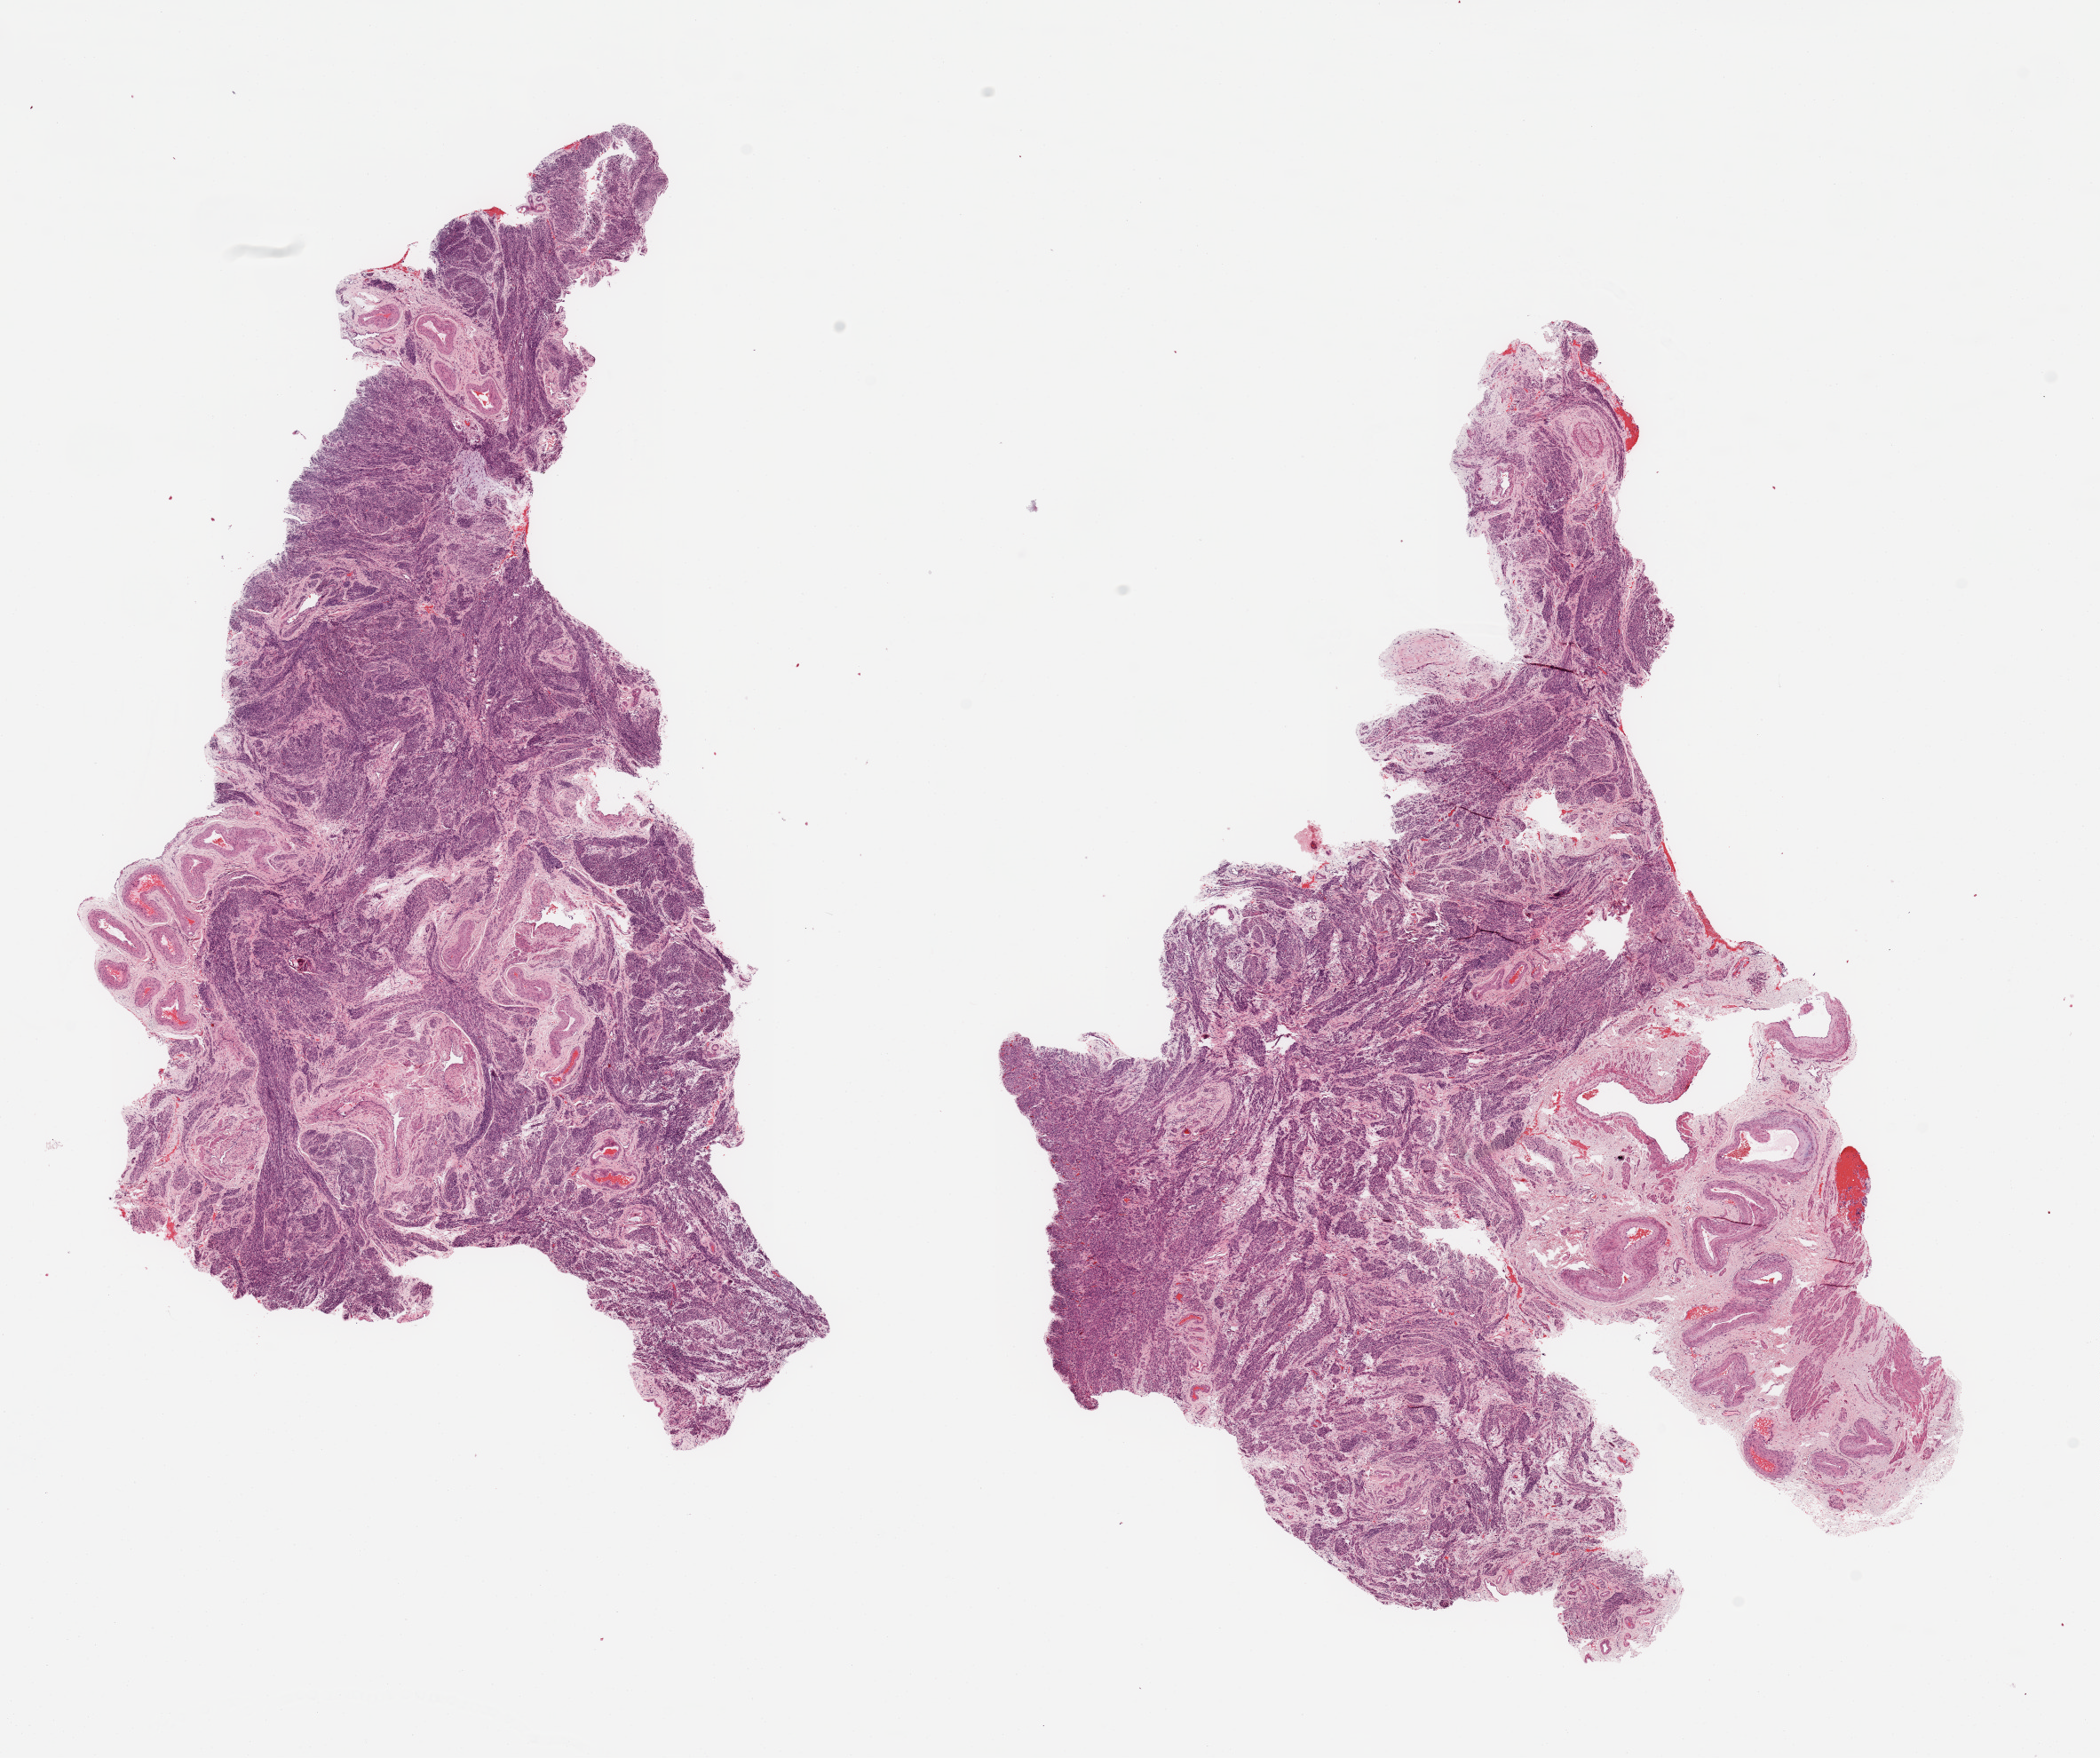
H&E whole-slide image — shown as a low-resolution overview of the whole scanned area (about 18.7 x 15.7 mm, acquisition: 20x scan), normal (non-tumour) tissue sample, uterus. 56-year-old female patient.
This section: normal (non-tumour) tissue from the same patient. Patient diagnosis: Endometrioid adenocarcinoma, NOS.